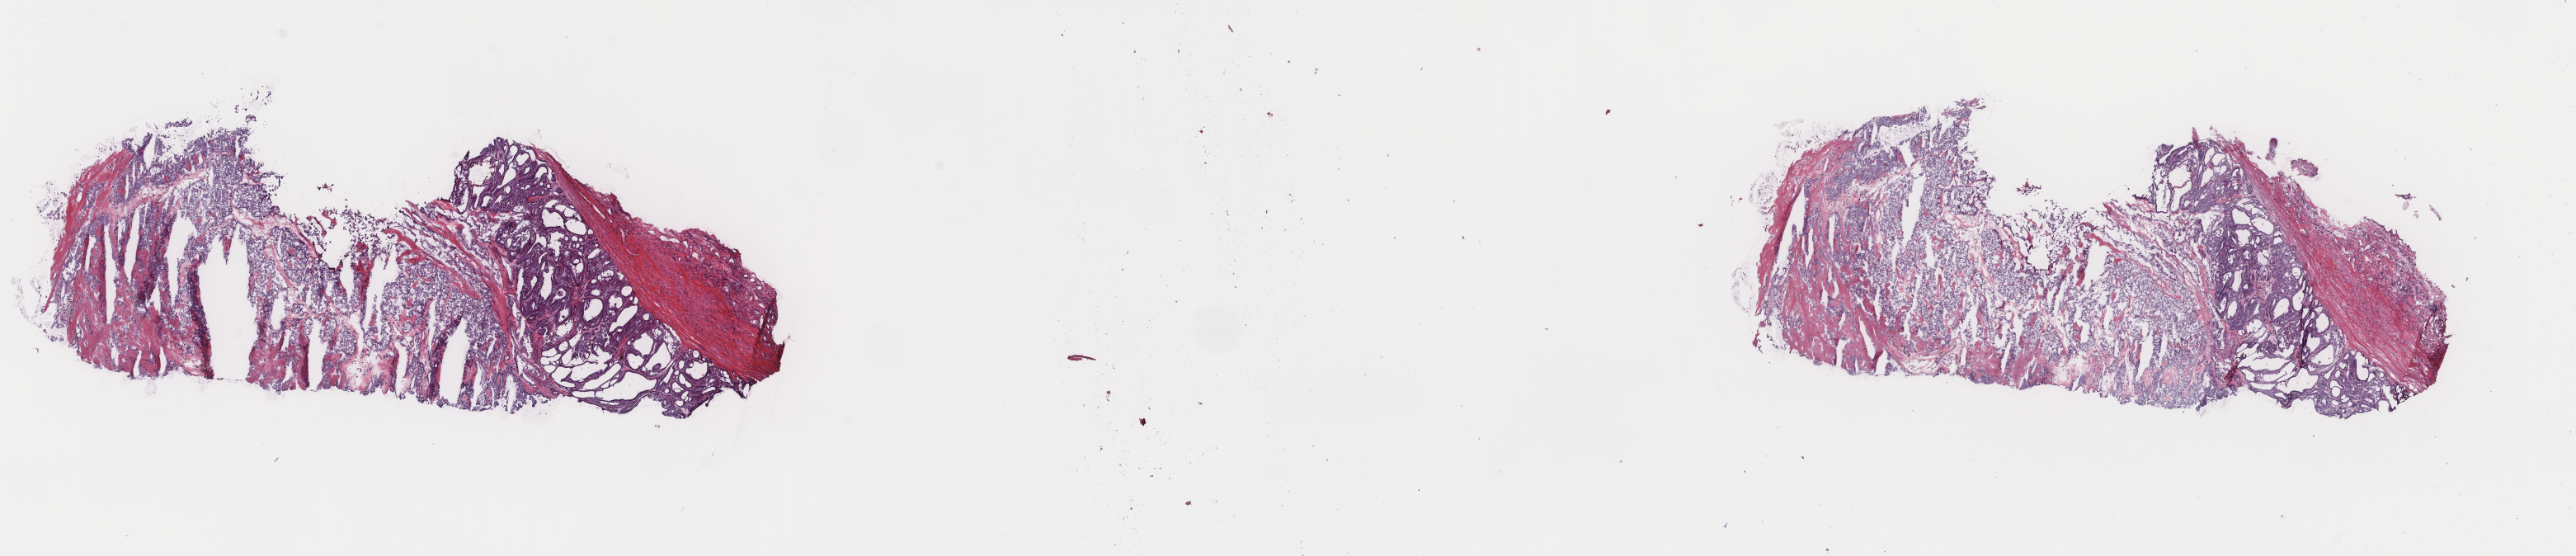
Whole-slide histology image, H&E, a low-resolution overview of the entire scanned area, about 24.8 x 5.4 mm (from a 40x scan), frozen section, sample: primary tumour, thyroid. Male, age 76 years at initial diagnosis. Composition of this section per pathologist review: tumour cells 70%, tumour nuclei 65%, normal cells 20%, stromal cells 10%, necrosis 0%. Inflammatory infiltration, as recorded: lymphocyte infiltration 0%, monocyte infiltration 0%, neutrophil infiltration 0%.
* laterality: bilateral
* histologic diagnosis: Papillary carcinoma, follicular variant (thyroid gland)
* AJCC pathologic stage: I (7th edition)